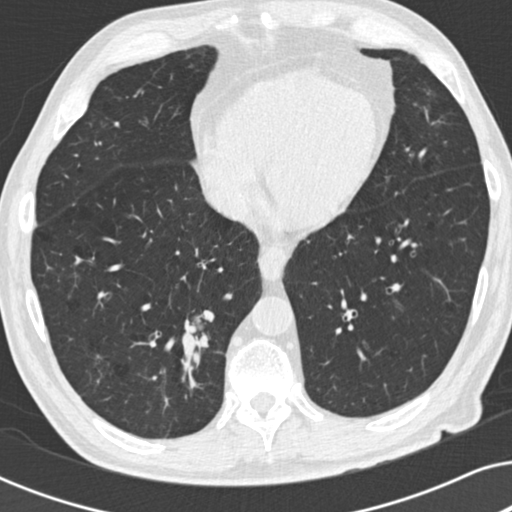
Chest CT (low-dose screening protocol), one axial image; baseline screening round; lung window (W 1500 / L -600 HU); 120 kVp. Male, age 73 years at enrolment. Current smoker at enrolment.
Expert-annotated lung lesion, box from (x=155, y=293) to (x=226, y=371) px. The screening reader recorded 2 non-calcified nodules or masses ≥4 mm on this exam (right lower lobe, right upper lobe); which of them this box marks is not recorded. Lung cancer was diagnosed 63 days after this screen: carcinoid tumor, NOS, right lower lobe, carcinoid, stage not assessed, 12 mm at pathology.